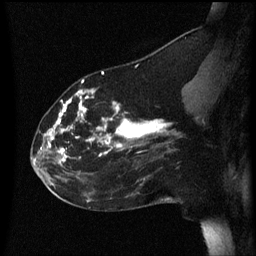
Breast MRI (dynamic contrast-enhanced), one sagittal slice. Slice 23 of 60 in the series (ordered by position). Dynamic contrast-enhanced series, image 2 of 3 at this slice position (ordered by acquisition). 1.5 T. TE 4.2 ms, TR 8.4 ms. 256 × 256 image matrix, field of view 200 × 200 mm. Patient: female, 35 years. Case-level facts recorded for this patient, not image findings: setting: breast cancer imaged before/during neoadjuvant chemotherapy; receptor status: HER2-positive.
Annotated regions visible in this slice (semi-automatic segmentation, software-assisted and operator-edited):
- analysis volume of interest (the breast-tissue region the enhancement analysis was run in; not a lesion): box from (x=32, y=72) to (x=178, y=173) px
- tumour enhancement mask (voxels above the 70 % enhancement threshold inside the analysis volume of interest): (x=41, y=72)–(x=173, y=161)